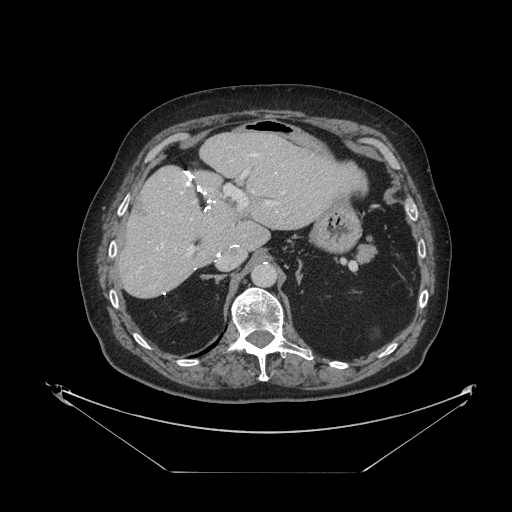
Contrast-enhanced abdominal CT, one axial slice; slice 68 of 121 in the series (ordered by position); reconstruction kernel STANDARD; soft-tissue window (W 400 / L 40 HU); 2.5 mm slice thickness; 512 × 512 image matrix. Male patient, age 68 years. From the clinical record (not read from this slice): diagnosis: colorectal cancer liver metastases, imaged before liver resection; multiple liver metastases: no.
Outlined on this slice (expert manual segmentation):
- hepatic veins: box from (x=158, y=154) to (x=285, y=250) px
- liver: (x=120, y=133)–(x=365, y=298)
- planned liver remnant (the part of the liver to remain after resection): (x=120, y=133)–(x=366, y=298)
- portal vein (with intrahepatic branches): (x=187, y=170)–(x=281, y=255)
- liver metastasis: (x=132, y=199)–(x=147, y=217)